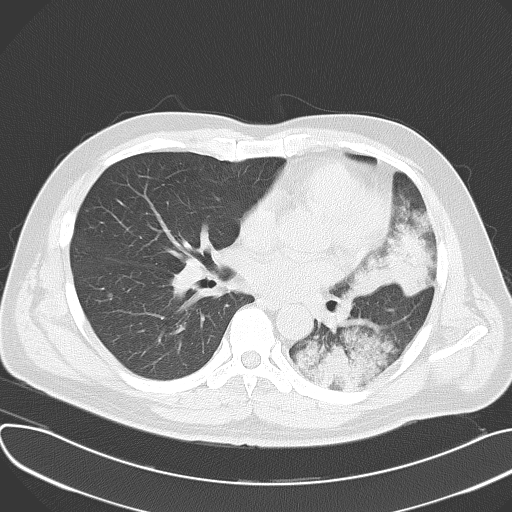
Chest CT, one axial slice; slice 32 of 62 in the series (ordered by position); 120 kVp; lung window (W 1500 / L -600 HU); 512 × 512 image matrix. Patient: male, 48 years. From the clinical record (not read from this slice): clinical TNM (as recorded): T4 N0 M0.
Structures marked on this image (rectangle marked by the reading radiologist):
- lung tumour (recorded histology: adenocarcinoma): bounding box <351,223,432,299> (left, top, right, bottom; pixels)